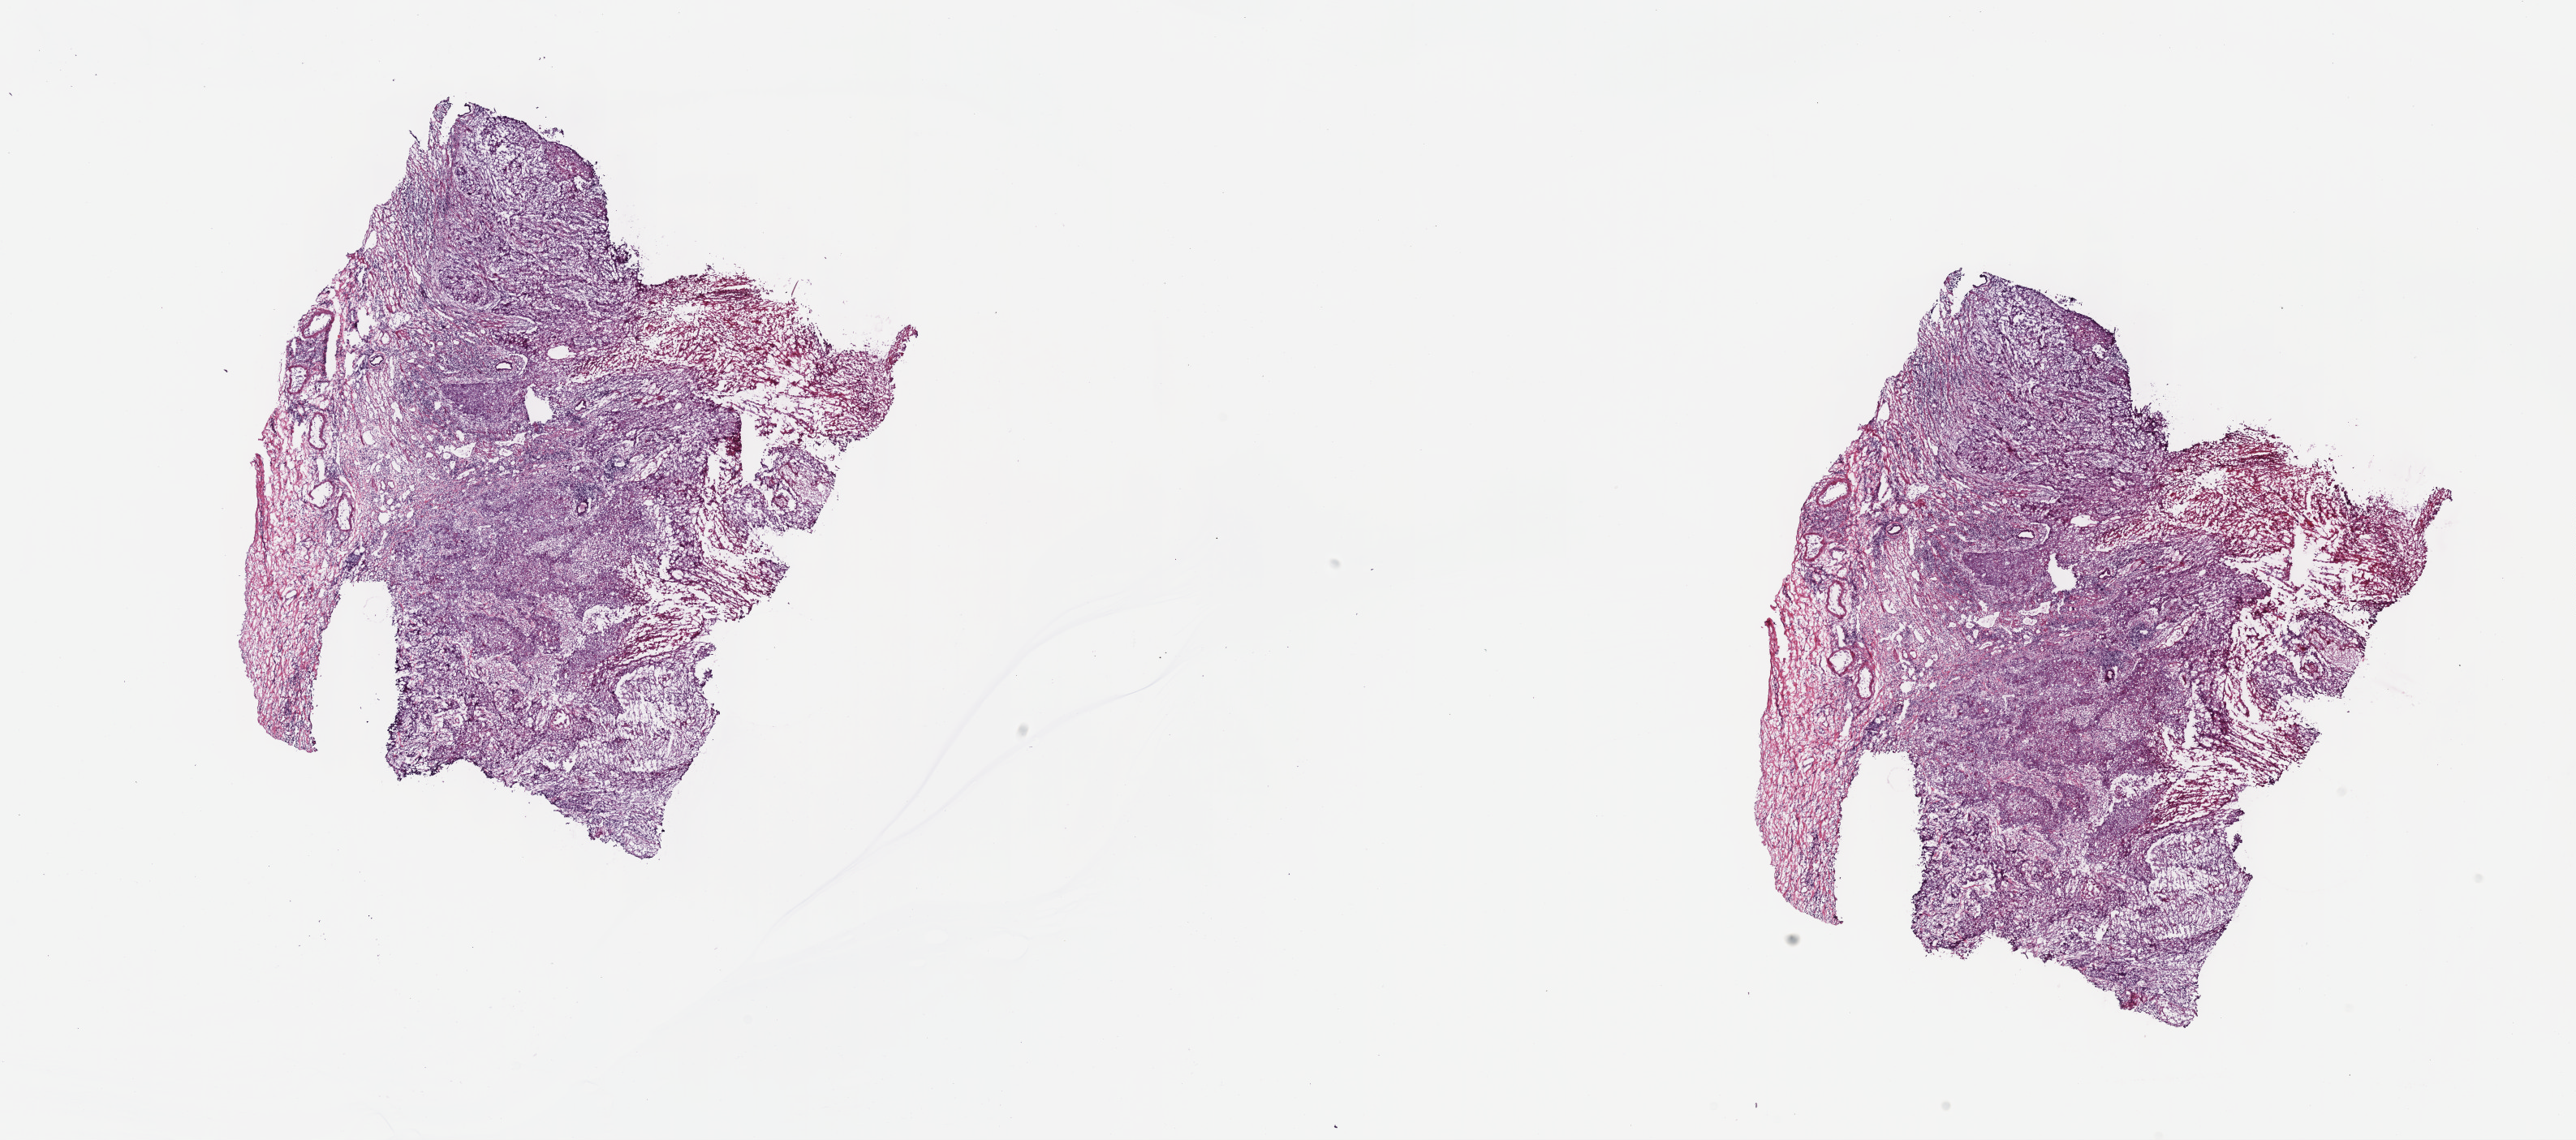
Digitized Hematoxylin and eosin (H&E) stained tissue section (whole slide), a low-resolution overview of the entire scanned area, about 25.7 x 11.4 mm, frozen section from the top of the tissue portion, primary tumour sample from the esophagus. Patient: male, age at initial diagnosis 53 years. Histologic grade: G2 (moderately differentiated). Composition of this section per pathologist review: tumour cells 75%, tumour nuclei 75%, normal cells 0%, stromal cells 17%, necrosis 8%. Inflammatory infiltration, as recorded: lymphocyte infiltration 2%, monocyte infiltration 2%, neutrophil infiltration 4%.
AJCC pathologic stage: IIB (7th edition). Pathologic diagnosis: Squamous cell carcinoma, NOS.